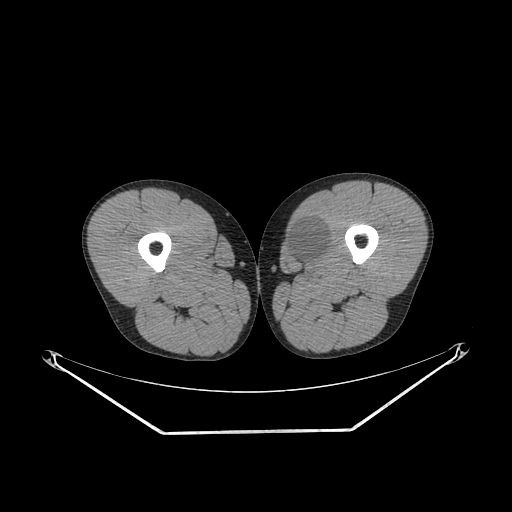
CT of an extremity soft-tissue mass (from a PET/CT study), one axial slice. Position 254 of 311 along the scan axis. 140 kVp. Soft-tissue window (W 400 / L 40 HU). 512 × 512 image matrix, field of view 500 × 500 mm. Male patient. From the clinical record (not read from this slice): histological type: mixoid liposarcoma; grade: low; site of the primary tumour: left thigh.
Outlined on this slice (expert contour drawn on MRI and transferred to this co-registered scan by the dataset authors):
- gross tumour volume (mass): bounding box (x1, y1, x2, y2) in pixels: (286, 219, 328, 264)